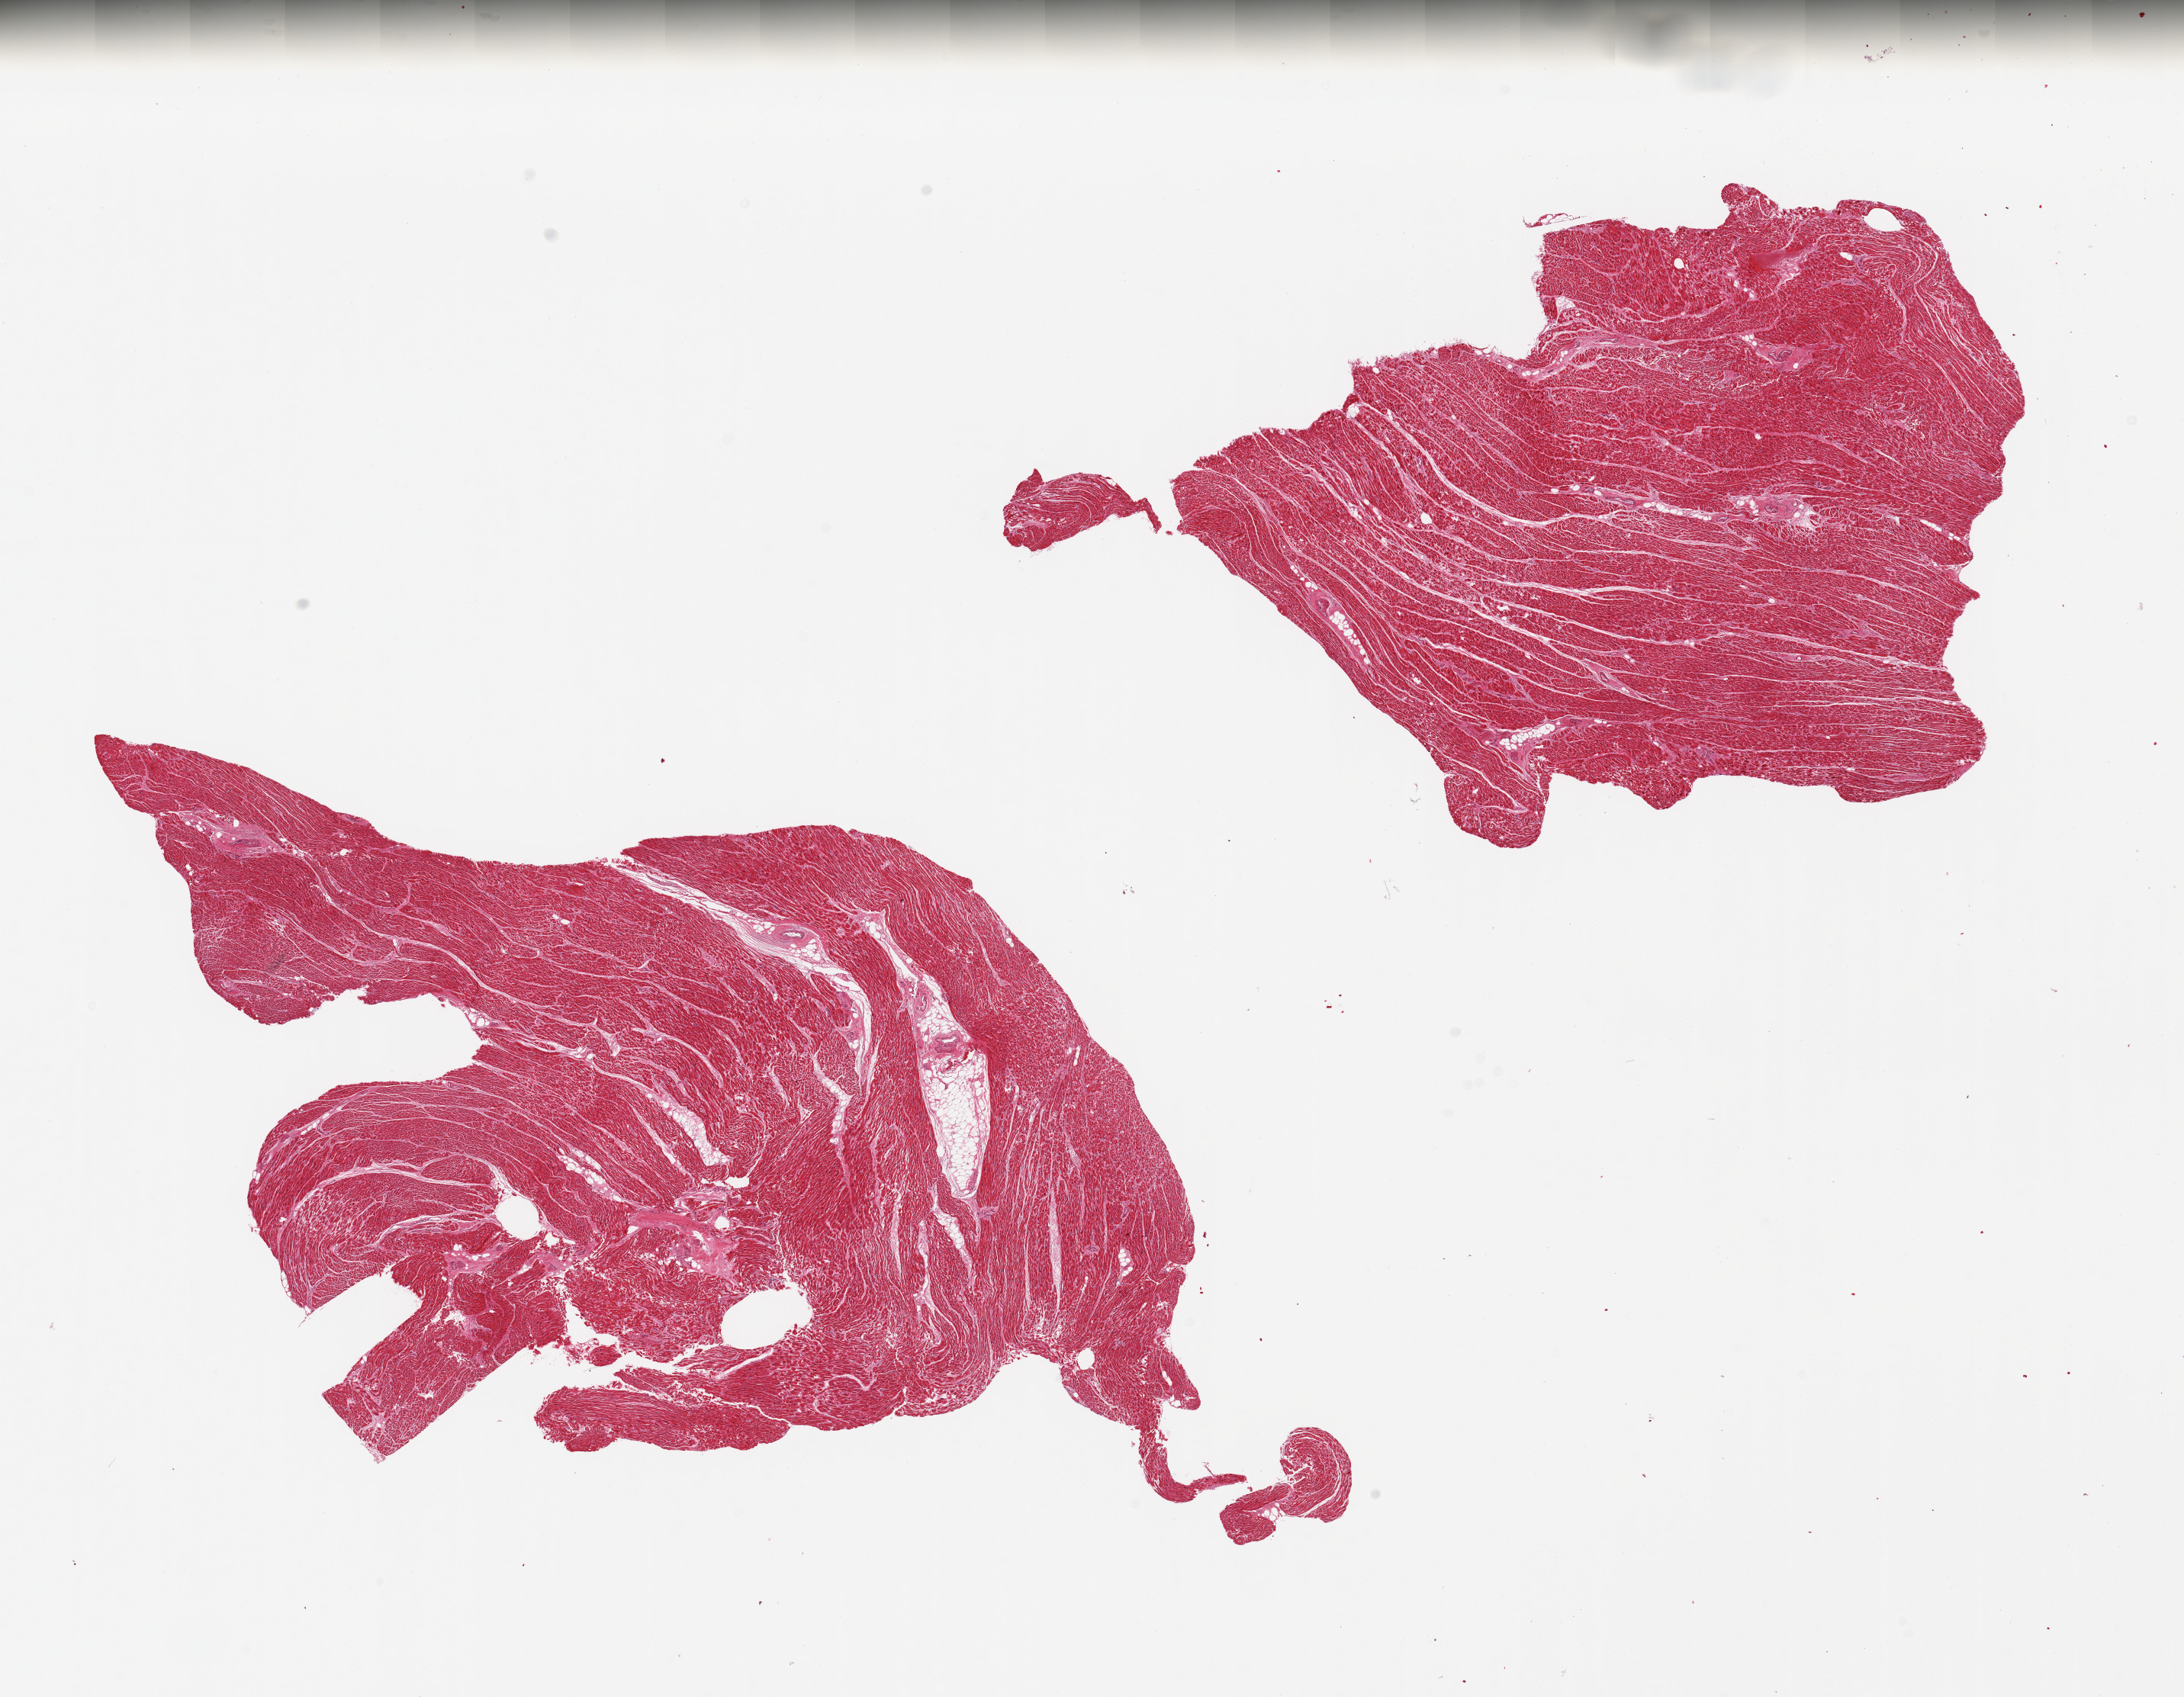
H&E whole-slide image, a low-resolution overview of the entire scanned area, about 22.6 x 17.6 mm. PAXgene-fixed, paraffin-embedded tissue. Sampled site (target tissue): heart. Tissue donor sample. Donor: female.
Review note (as recorded): 2 pieces.